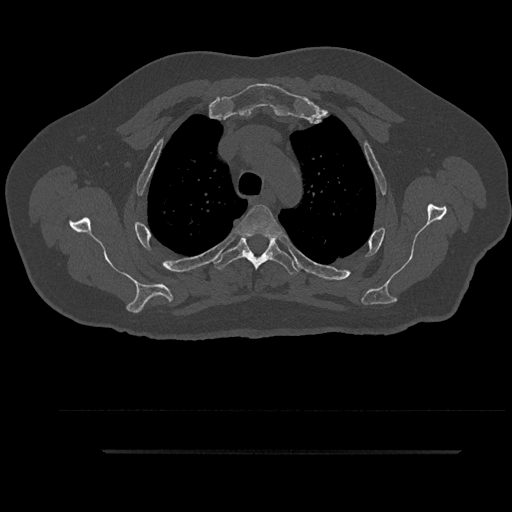
CT including the spine, one axial slice. Slice 692 of 797 in the series (ordered by position). 120 kVp. Bone window (W 1800 / L 400 HU). 512 × 512 image matrix. Male patient, age 63 years. From the clinical record (not read from this slice): primary cancer: renal; vertebrae with lytic lesions (as recorded): T8.
Outlined on this slice (semi-automatic segmentation, software-assisted and operator-edited):
- T3 vertebra: bounding box <236,205,282,239> (left, top, right, bottom; pixels)
- T4 vertebra: <213,236,300,274>